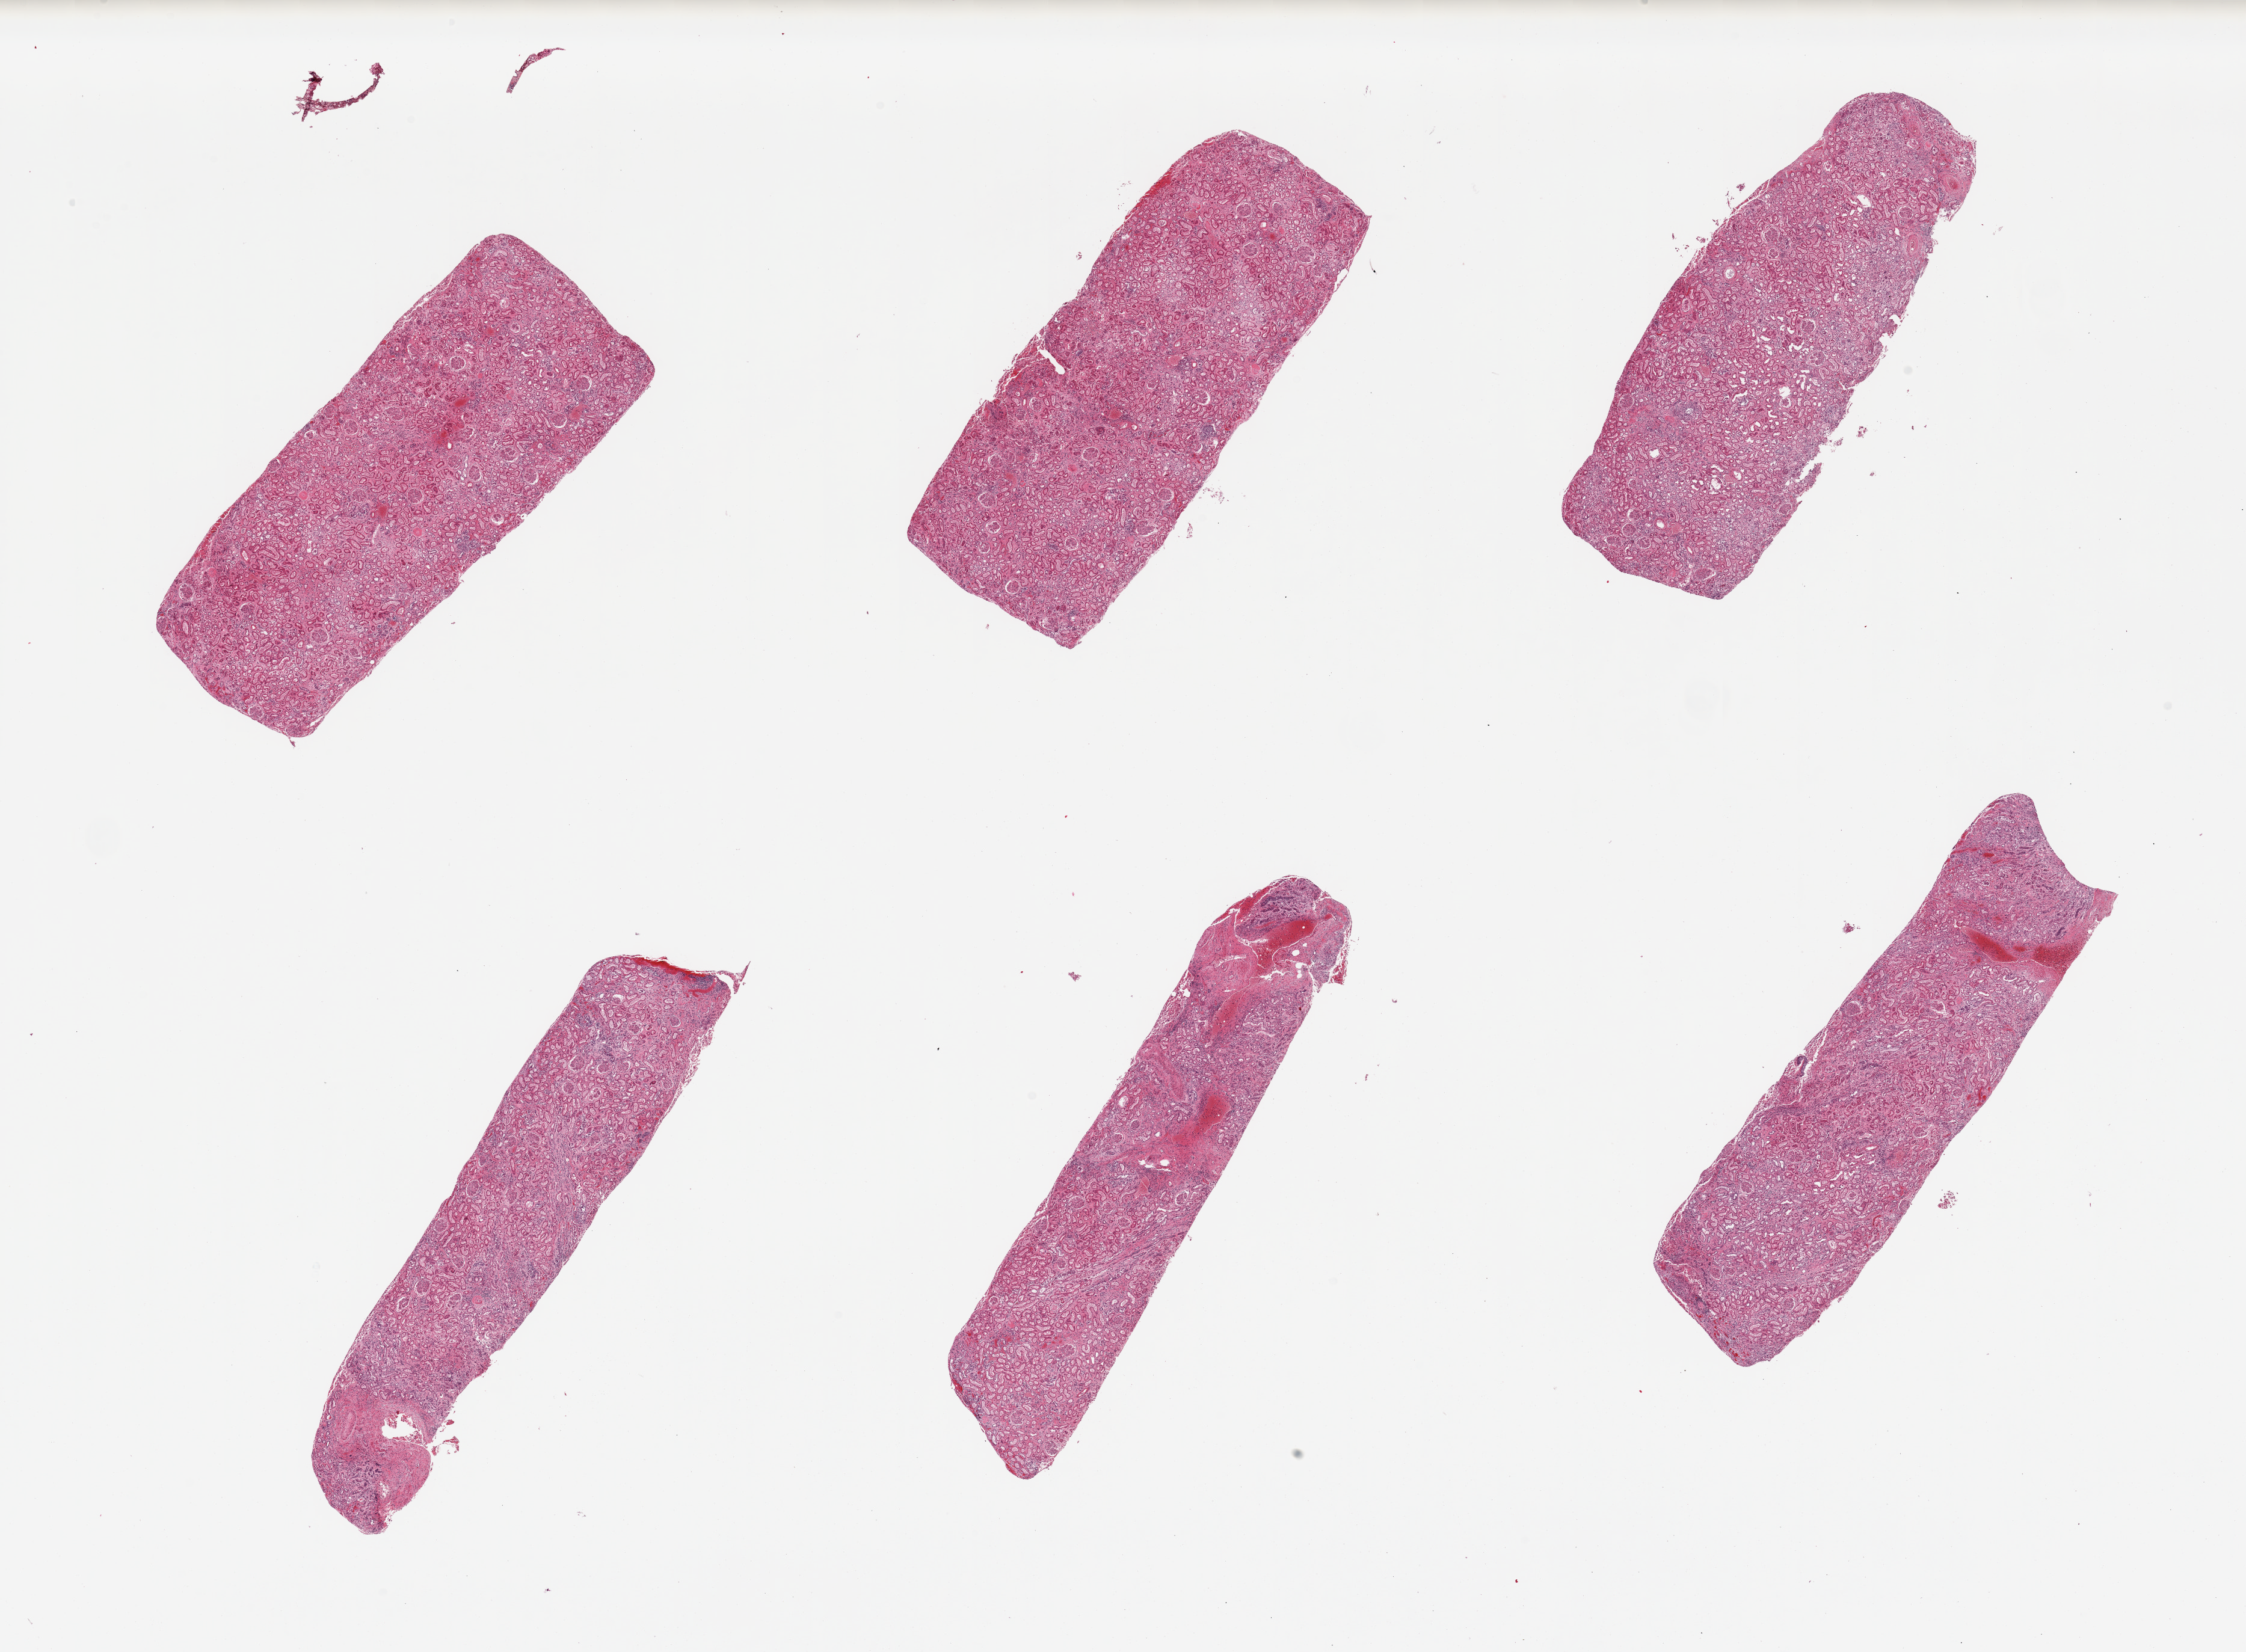
Digitized hematoxylin and eosin (H&E)-stained section — low-resolution overview of the scanned area, about 29.5 x 21.7 mm (slide scanned at 20x); PAXgene-fixed, paraffin-embedded tissue; sampled site (target tissue): renal cortex; tissue donor sample.
* pathologist's review note for this sample: 6 pieces, some interstitial fibrosis